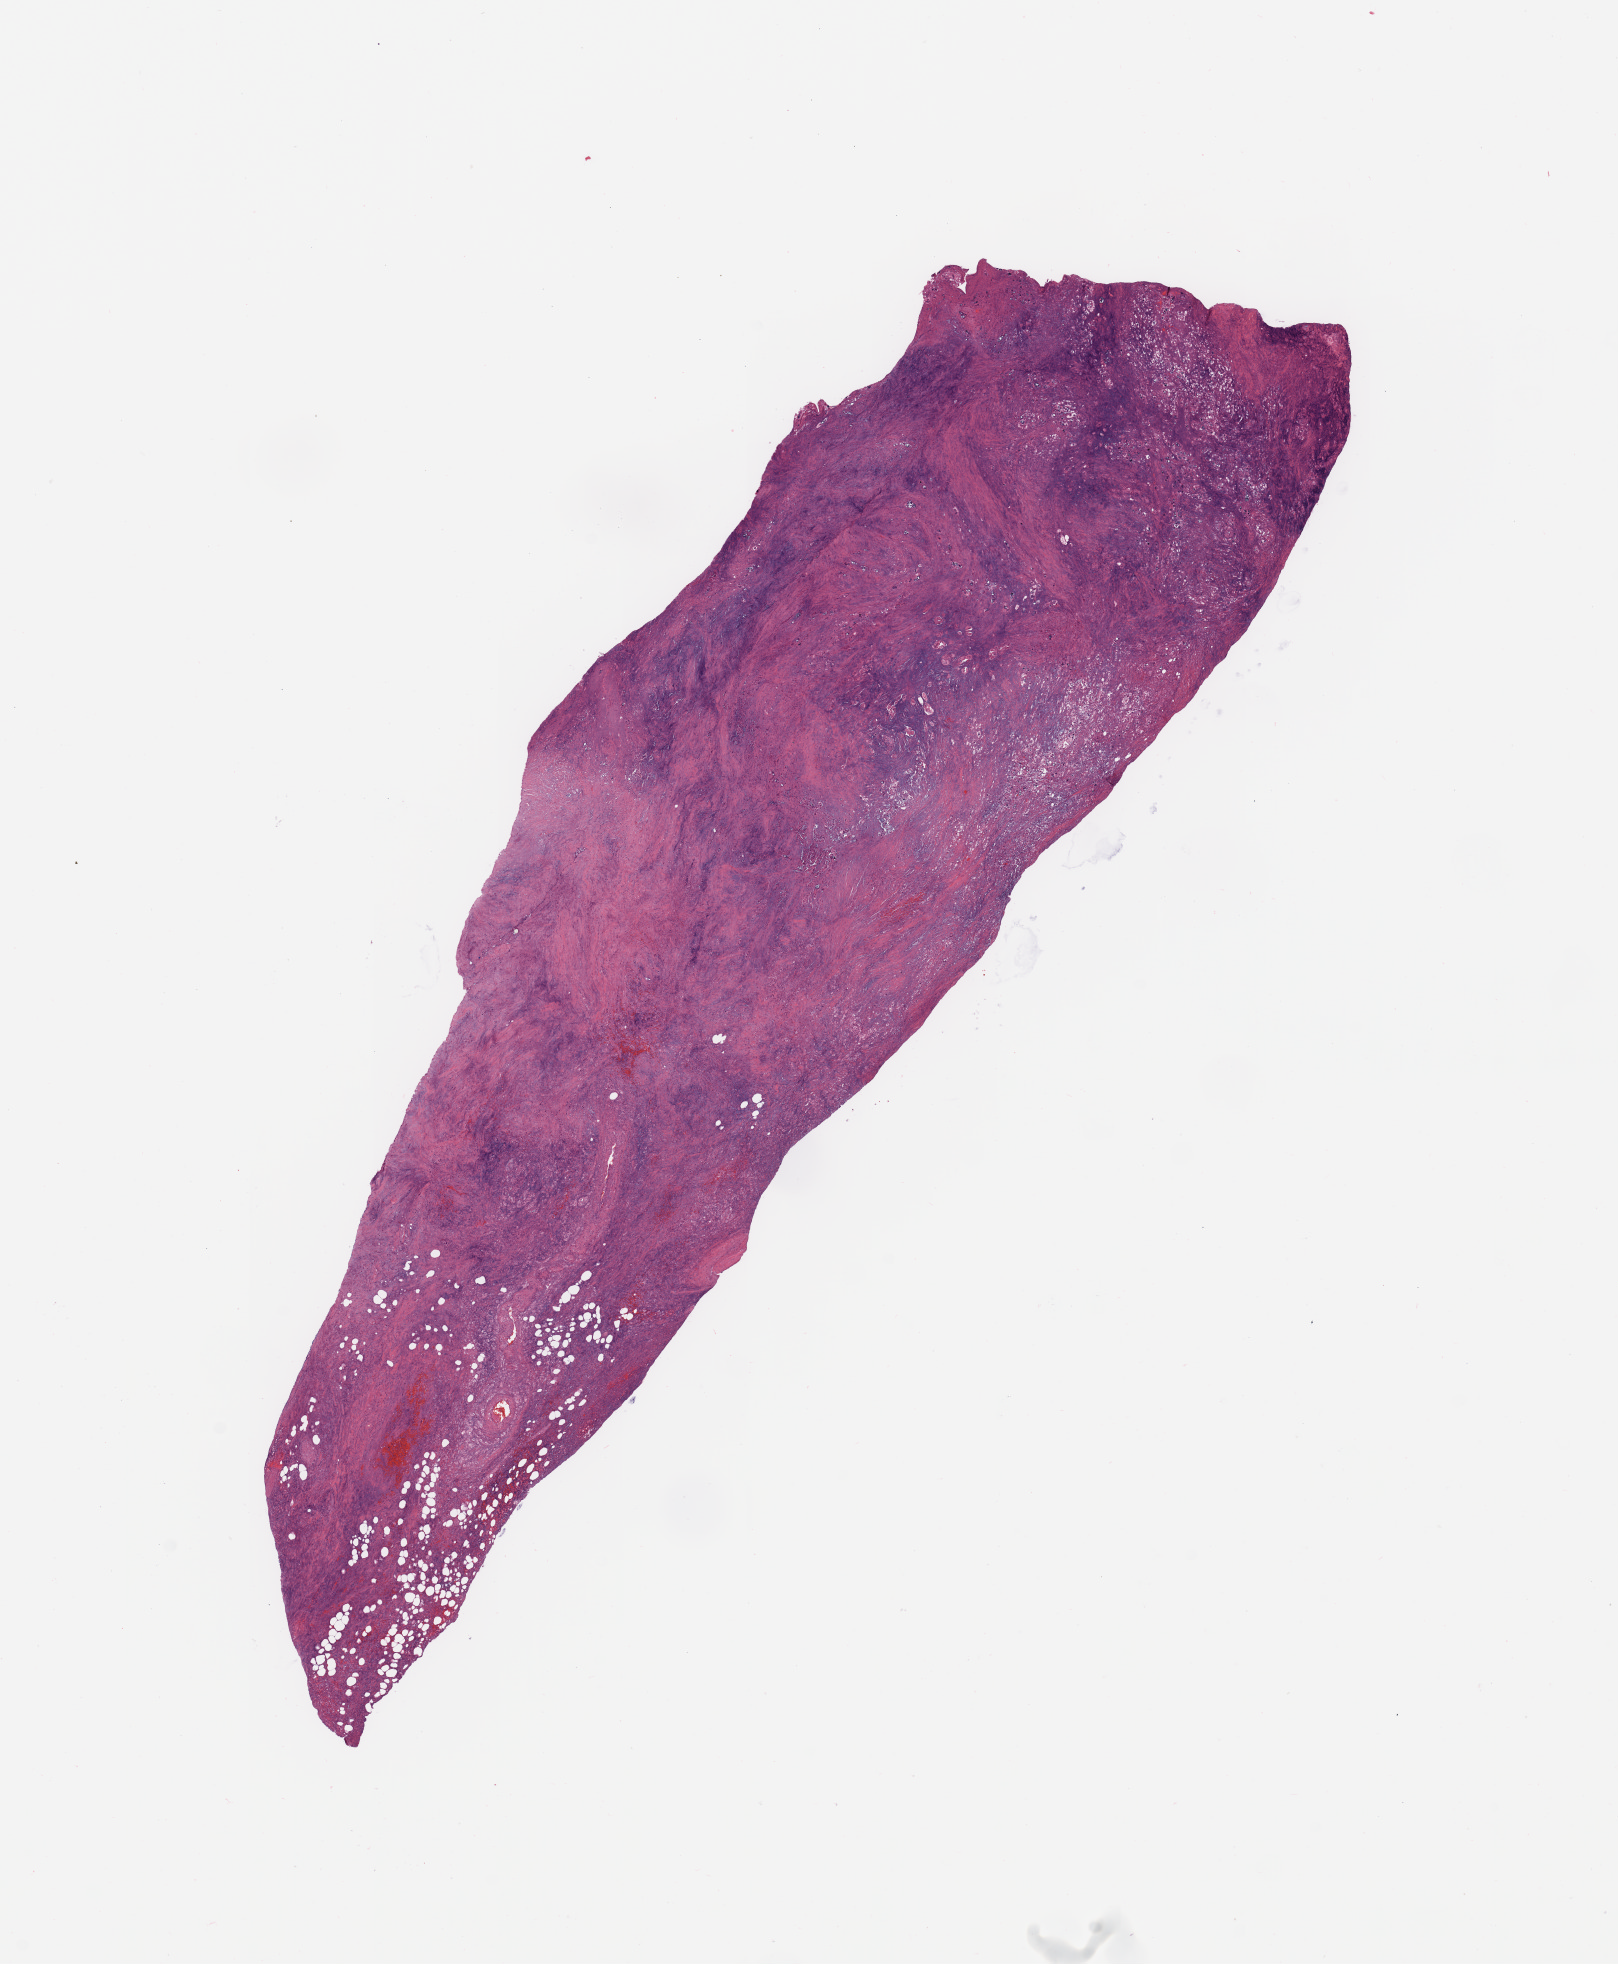
H&E whole-slide image, shown as a low-resolution overview of the whole scanned area (about 12.8 x 15.5 mm). Pancreas, tumour tissue. Male, 71 y/o. Histologic grade: G3 (poorly differentiated).
AJCC pathologic stage: IIB. Primary tumour site (as recorded): head. Histologic diagnosis: Infiltrating duct carcinoma, NOS.